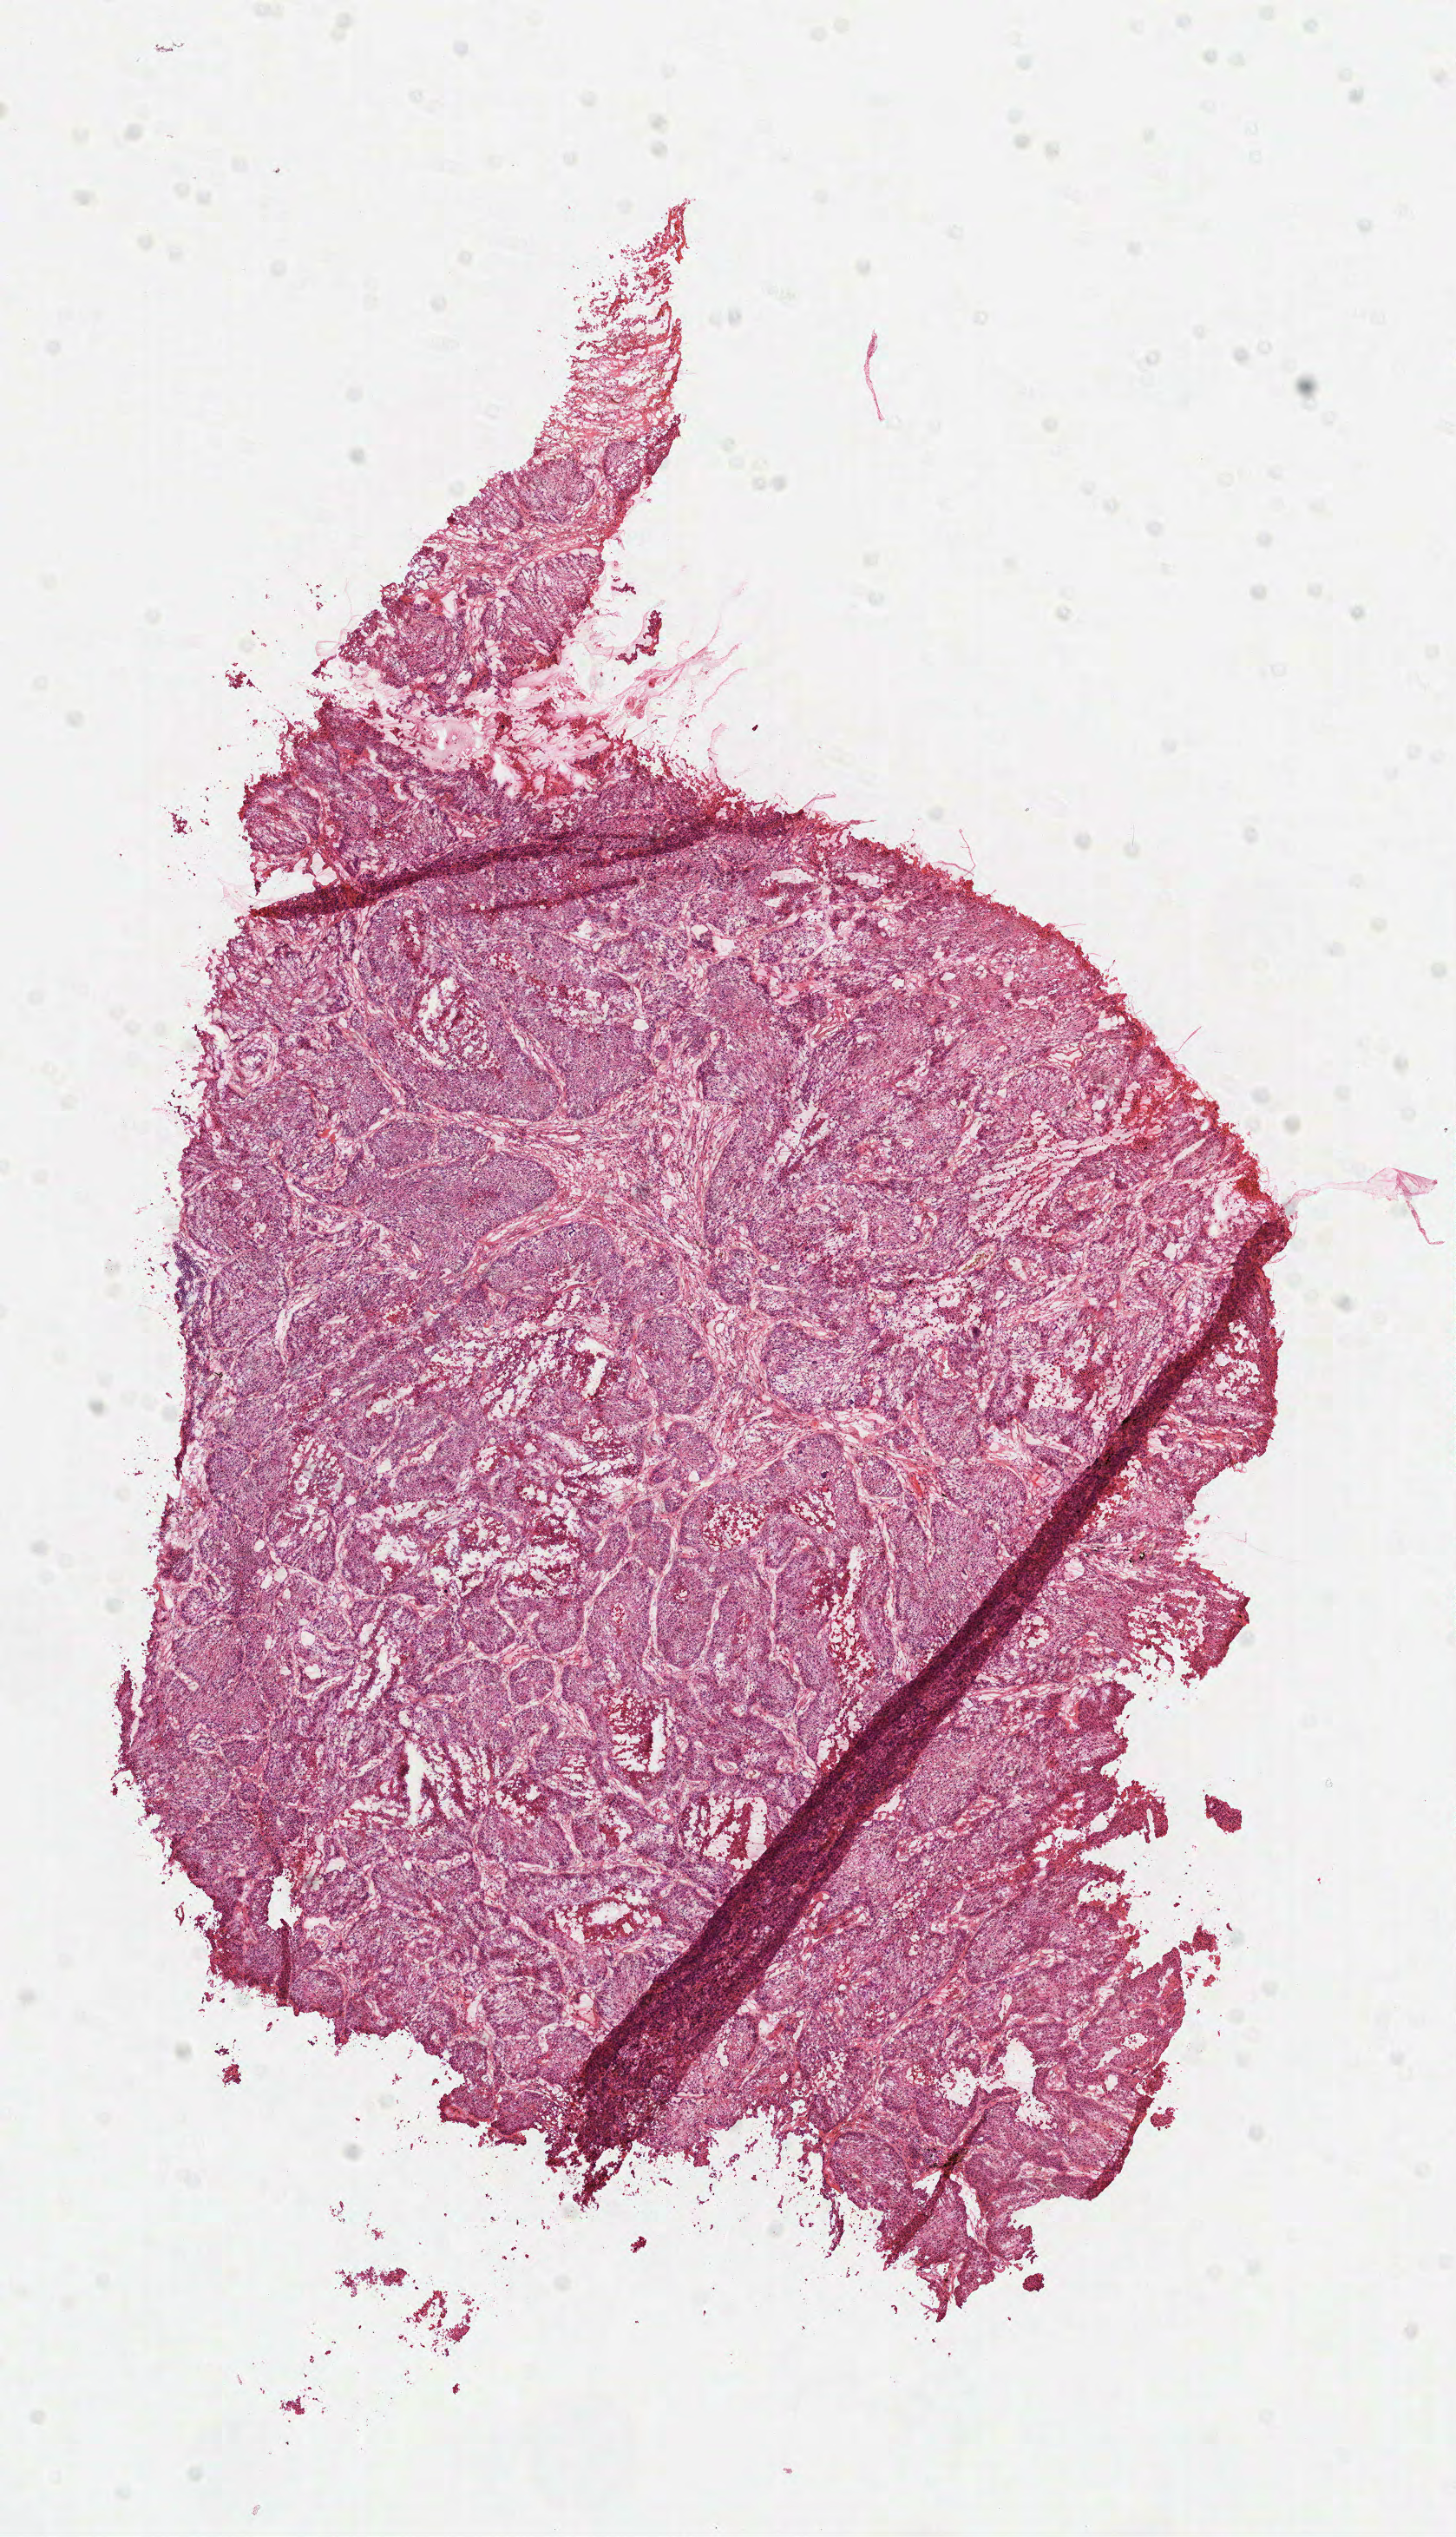
Whole-slide histology image, H&E, shown as a low-resolution overview of the whole scanned area (about 6.8 x 11.8 mm), formalin-fixed paraffin-embedded (FFPE) diagnostic section, sample: primary tumour, lung. Male, age 57 years at initial diagnosis.
Histologic diagnosis: Squamous cell carcinoma, NOS (lower lobe, lung). AJCC pathologic stage: IIB.